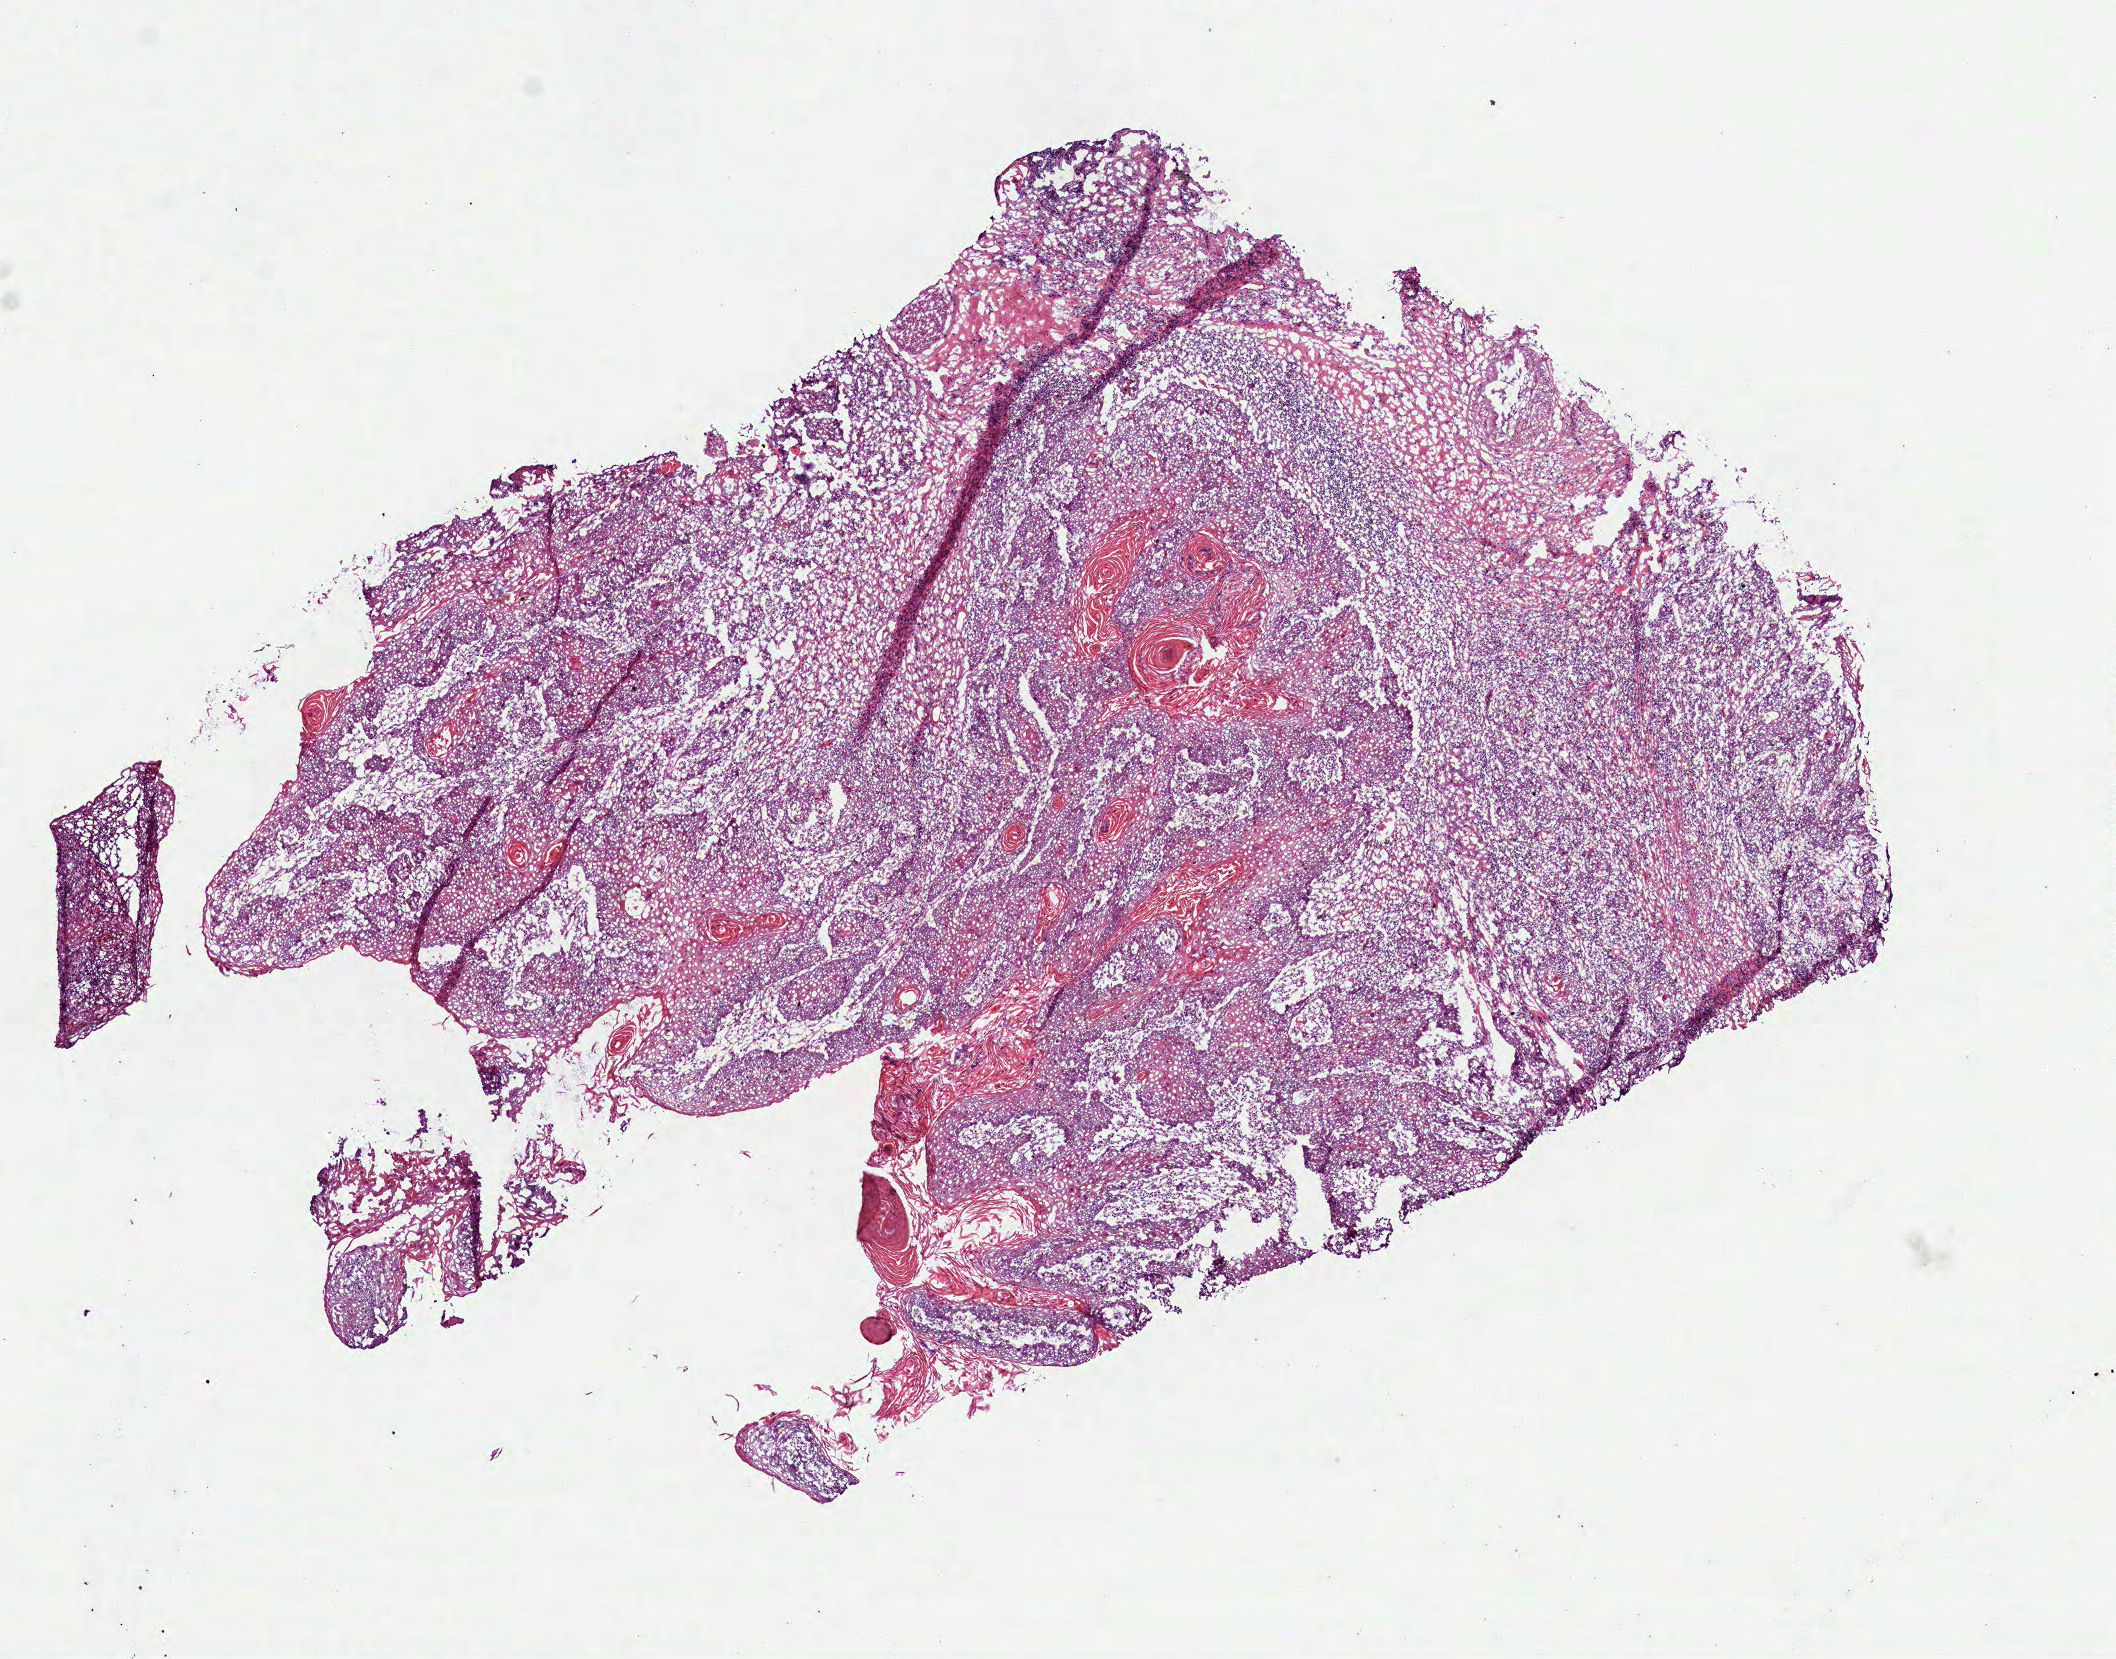
H&E-stained whole-slide image, low-resolution overview of the scanned area, about 8.5 x 6.7 mm; frozen section from the bottom of the tissue portion; primary tumour sample from the head and neck. Male patient; age at initial diagnosis 69 years. Histologic grade: G2 (moderately differentiated). Slide review estimates, as recorded: tumour cells 75%, tumour nuclei 70%, normal cells 0%, stromal cells 25%, necrosis 0%.
AJCC pathologic stage: III. Diagnosis: Squamous cell carcinoma, NOS. Lymph nodes positive (case pathology): 0 of 42 examined.